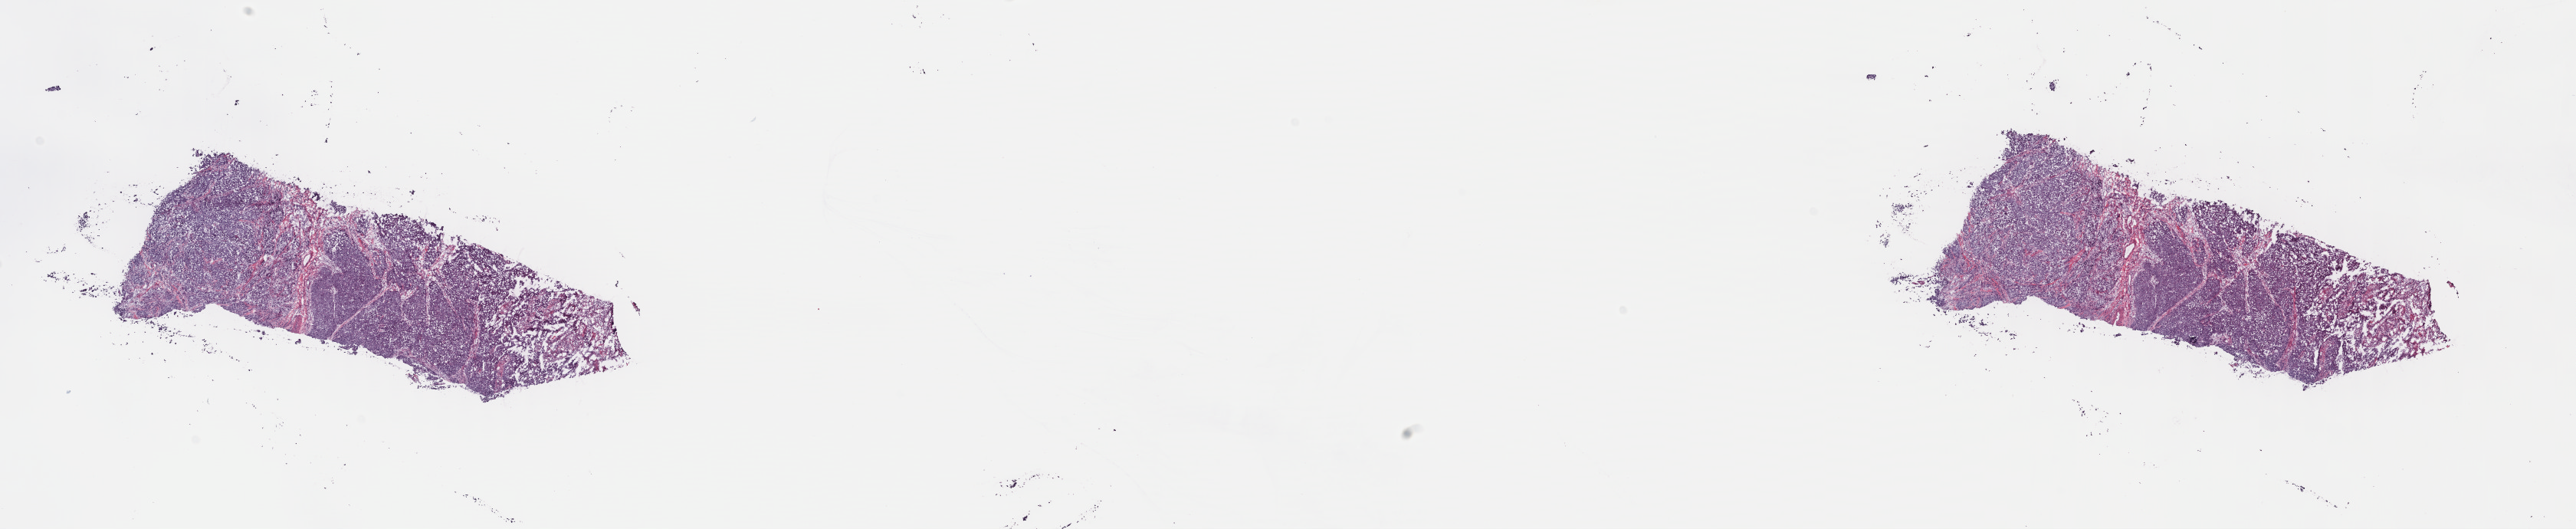
Hematoxylin and eosin (H&E) stained whole-slide image — whole scanned area (about 26.4 x 5.4 mm, from a 40x scan) shown as a low-resolution overview; frozen section; sample: primary tumour, cervix. Female patient; age at initial diagnosis 56 years. Histologic grade: G2 (moderately differentiated). Pathologist review of this section (percent, as recorded): tumour cells 80%, tumour nuclei 90%, normal cells 10%, stromal cells 10%, necrosis 0%. Infiltration values recorded for this section: lymphocyte infiltration 0%, monocyte infiltration 0%, neutrophil infiltration 0%.
- histologic diagnosis: Squamous cell carcinoma, NOS (cervix uteri)
- FIGO stage: IB1